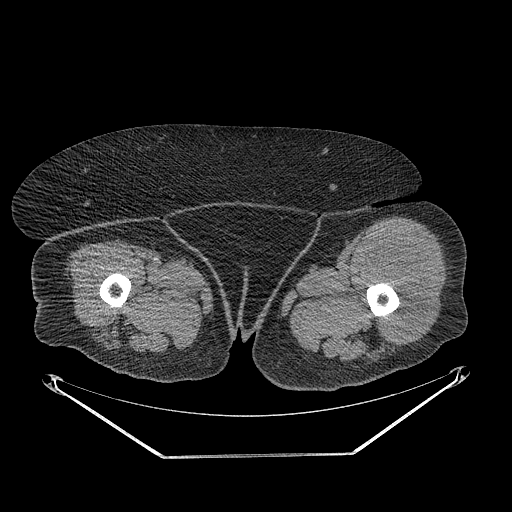
CT of an extremity soft-tissue mass (from a PET/CT study), one axial slice. Position 249 of 267 along the scan axis. Reconstruction kernel STANDARD. Soft-tissue window (W 400 / L 40 HU). 512 × 512 image matrix. Female patient. Case-level facts recorded for this patient, not image findings: histological type: undifferentiated – high grade; grade: high; site of the primary tumour: left thigh.
Annotated regions visible in this slice (expert contour drawn on MRI and transferred to this co-registered scan by the dataset authors):
- gross tumour volume including surrounding oedema: bounding box <363,238,430,343> (left, top, right, bottom; pixels)
- gross tumour volume (mass): <365,242,430,343>